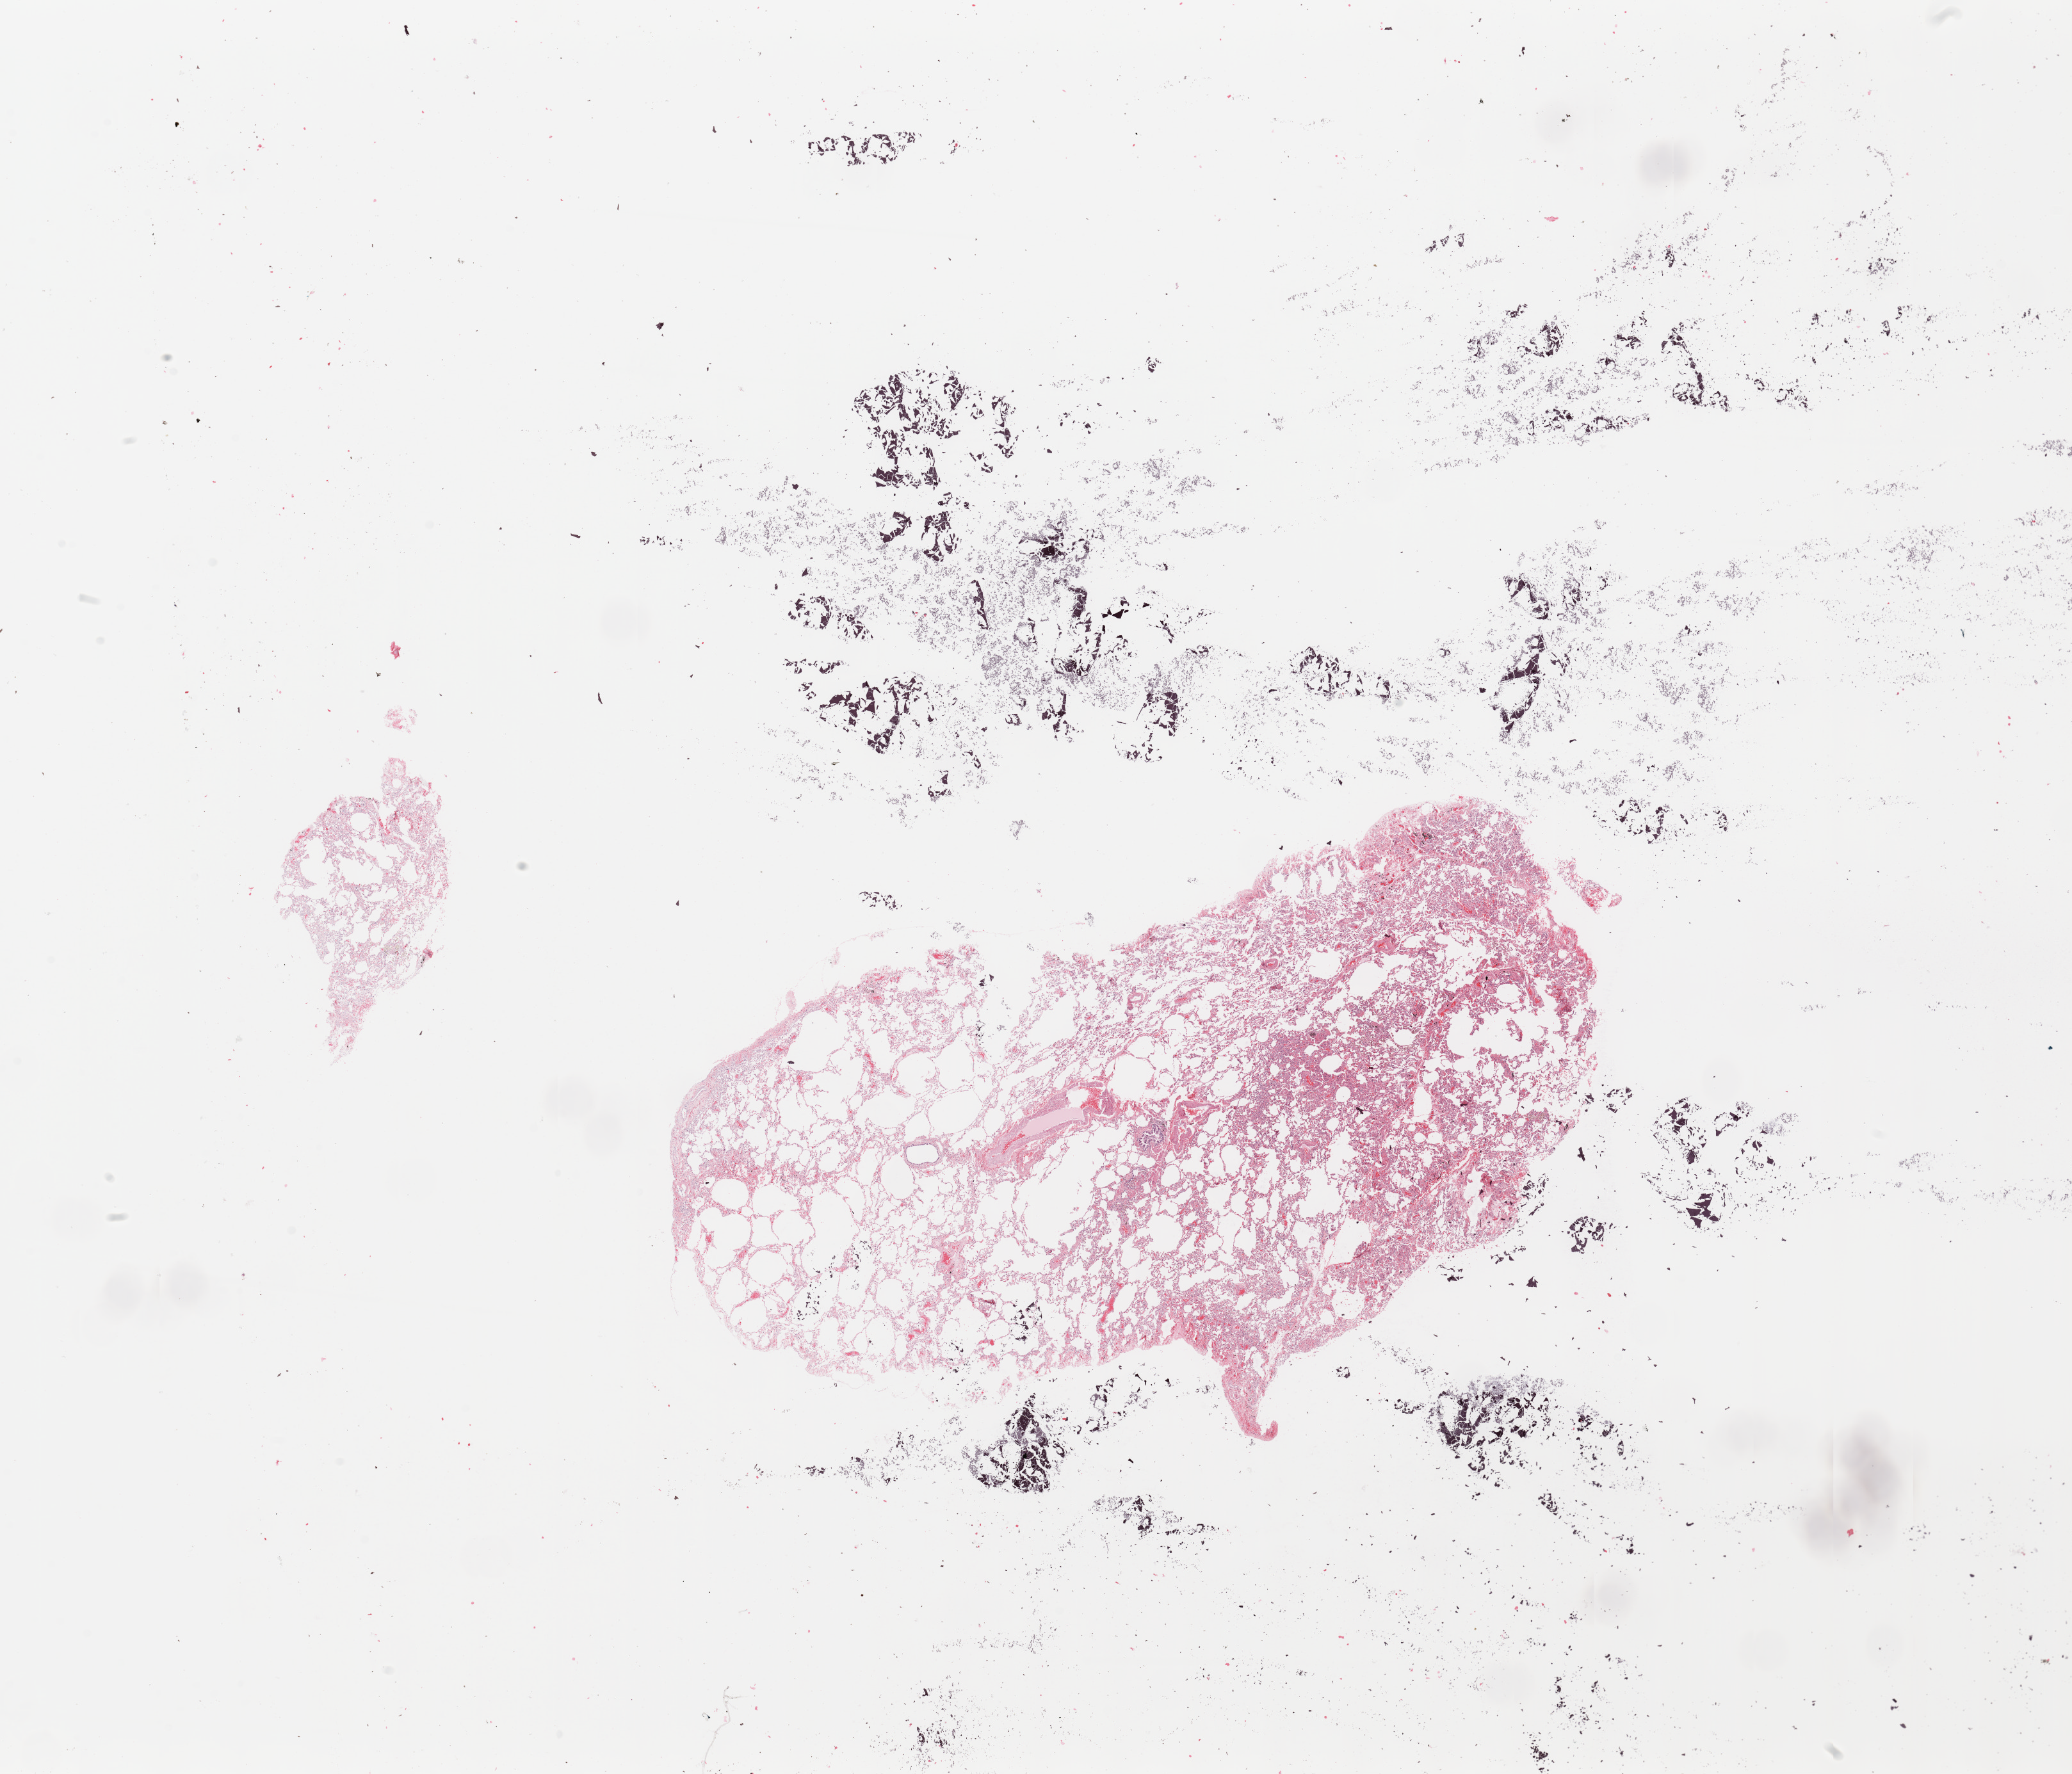
Hematoxylin and eosin (H&E) stained whole-slide image — shown as a low-resolution overview of the whole scanned area (about 25.6 x 21.9 mm); normal (non-tumour) tissue sample, sampled site: lung. Male, 64 y/o.
* this section: normal (non-tumour) tissue from the same patient
* patient diagnosis: Adenocarcinoma, NOS